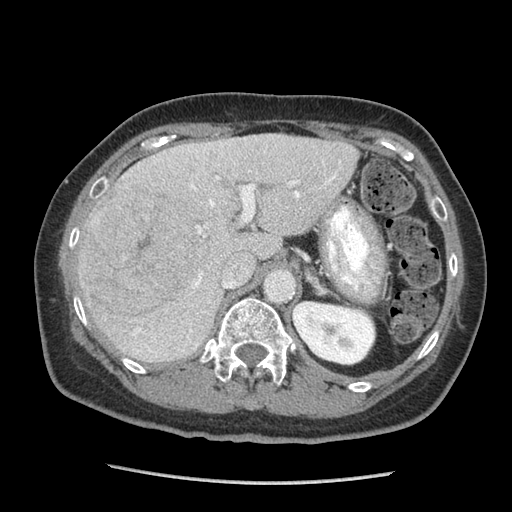
Contrast-enhanced abdominal CT (liver protocol), one axial slice; reconstruction kernel STANDARD; 140 kVp; soft-tissue window (W 400 / L 40 HU); 512 × 512 image matrix. Case-level facts recorded for this patient, not image findings: diagnosis: hepatocellular carcinoma (patient treated with transarterial chemoembolisation; whether this scan precedes or follows treatment is not stated here); TNM stage (as recorded): Stage-I; Child-Pugh class: A; tumour nodularity: uninodular.
Structures marked on this image (semi-automatic segmentation, software-assisted and operator-edited):
- liver parenchyma outside the tumour (the mass and vessels are separate outlines, so this box may not span the whole liver): bounding box <76,134,358,362> (left, top, right, bottom; pixels)
- mass: <81,186,211,327>
- liver vessels: <133,143,336,352>